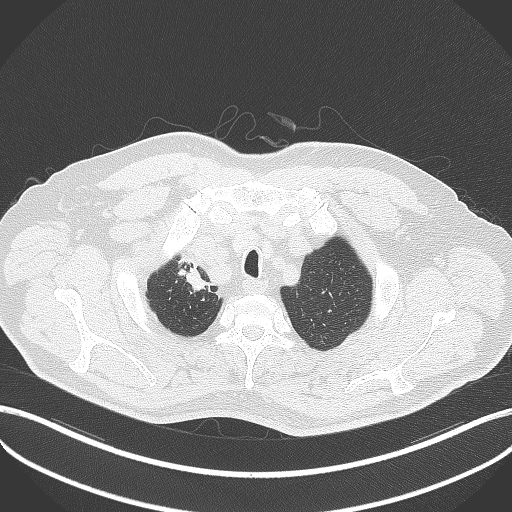
Chest CT, one axial slice; position 343 of 411 along the scan axis; reconstruction kernel B70f; 120 kVp; lung window (W 1500 / L -600 HU); 512 × 512 image matrix, field of view 400 × 400 mm. Patient: male, 60 years. Case-level facts recorded for this patient, not image findings: clinical TNM (as recorded): T1b N1 M0.
Annotated regions visible in this slice (rectangle marked by the reading radiologist):
- lung tumour (recorded histology: squamous cell carcinoma): bounding box [x1, y1, x2, y2] px = [184, 261, 212, 296]